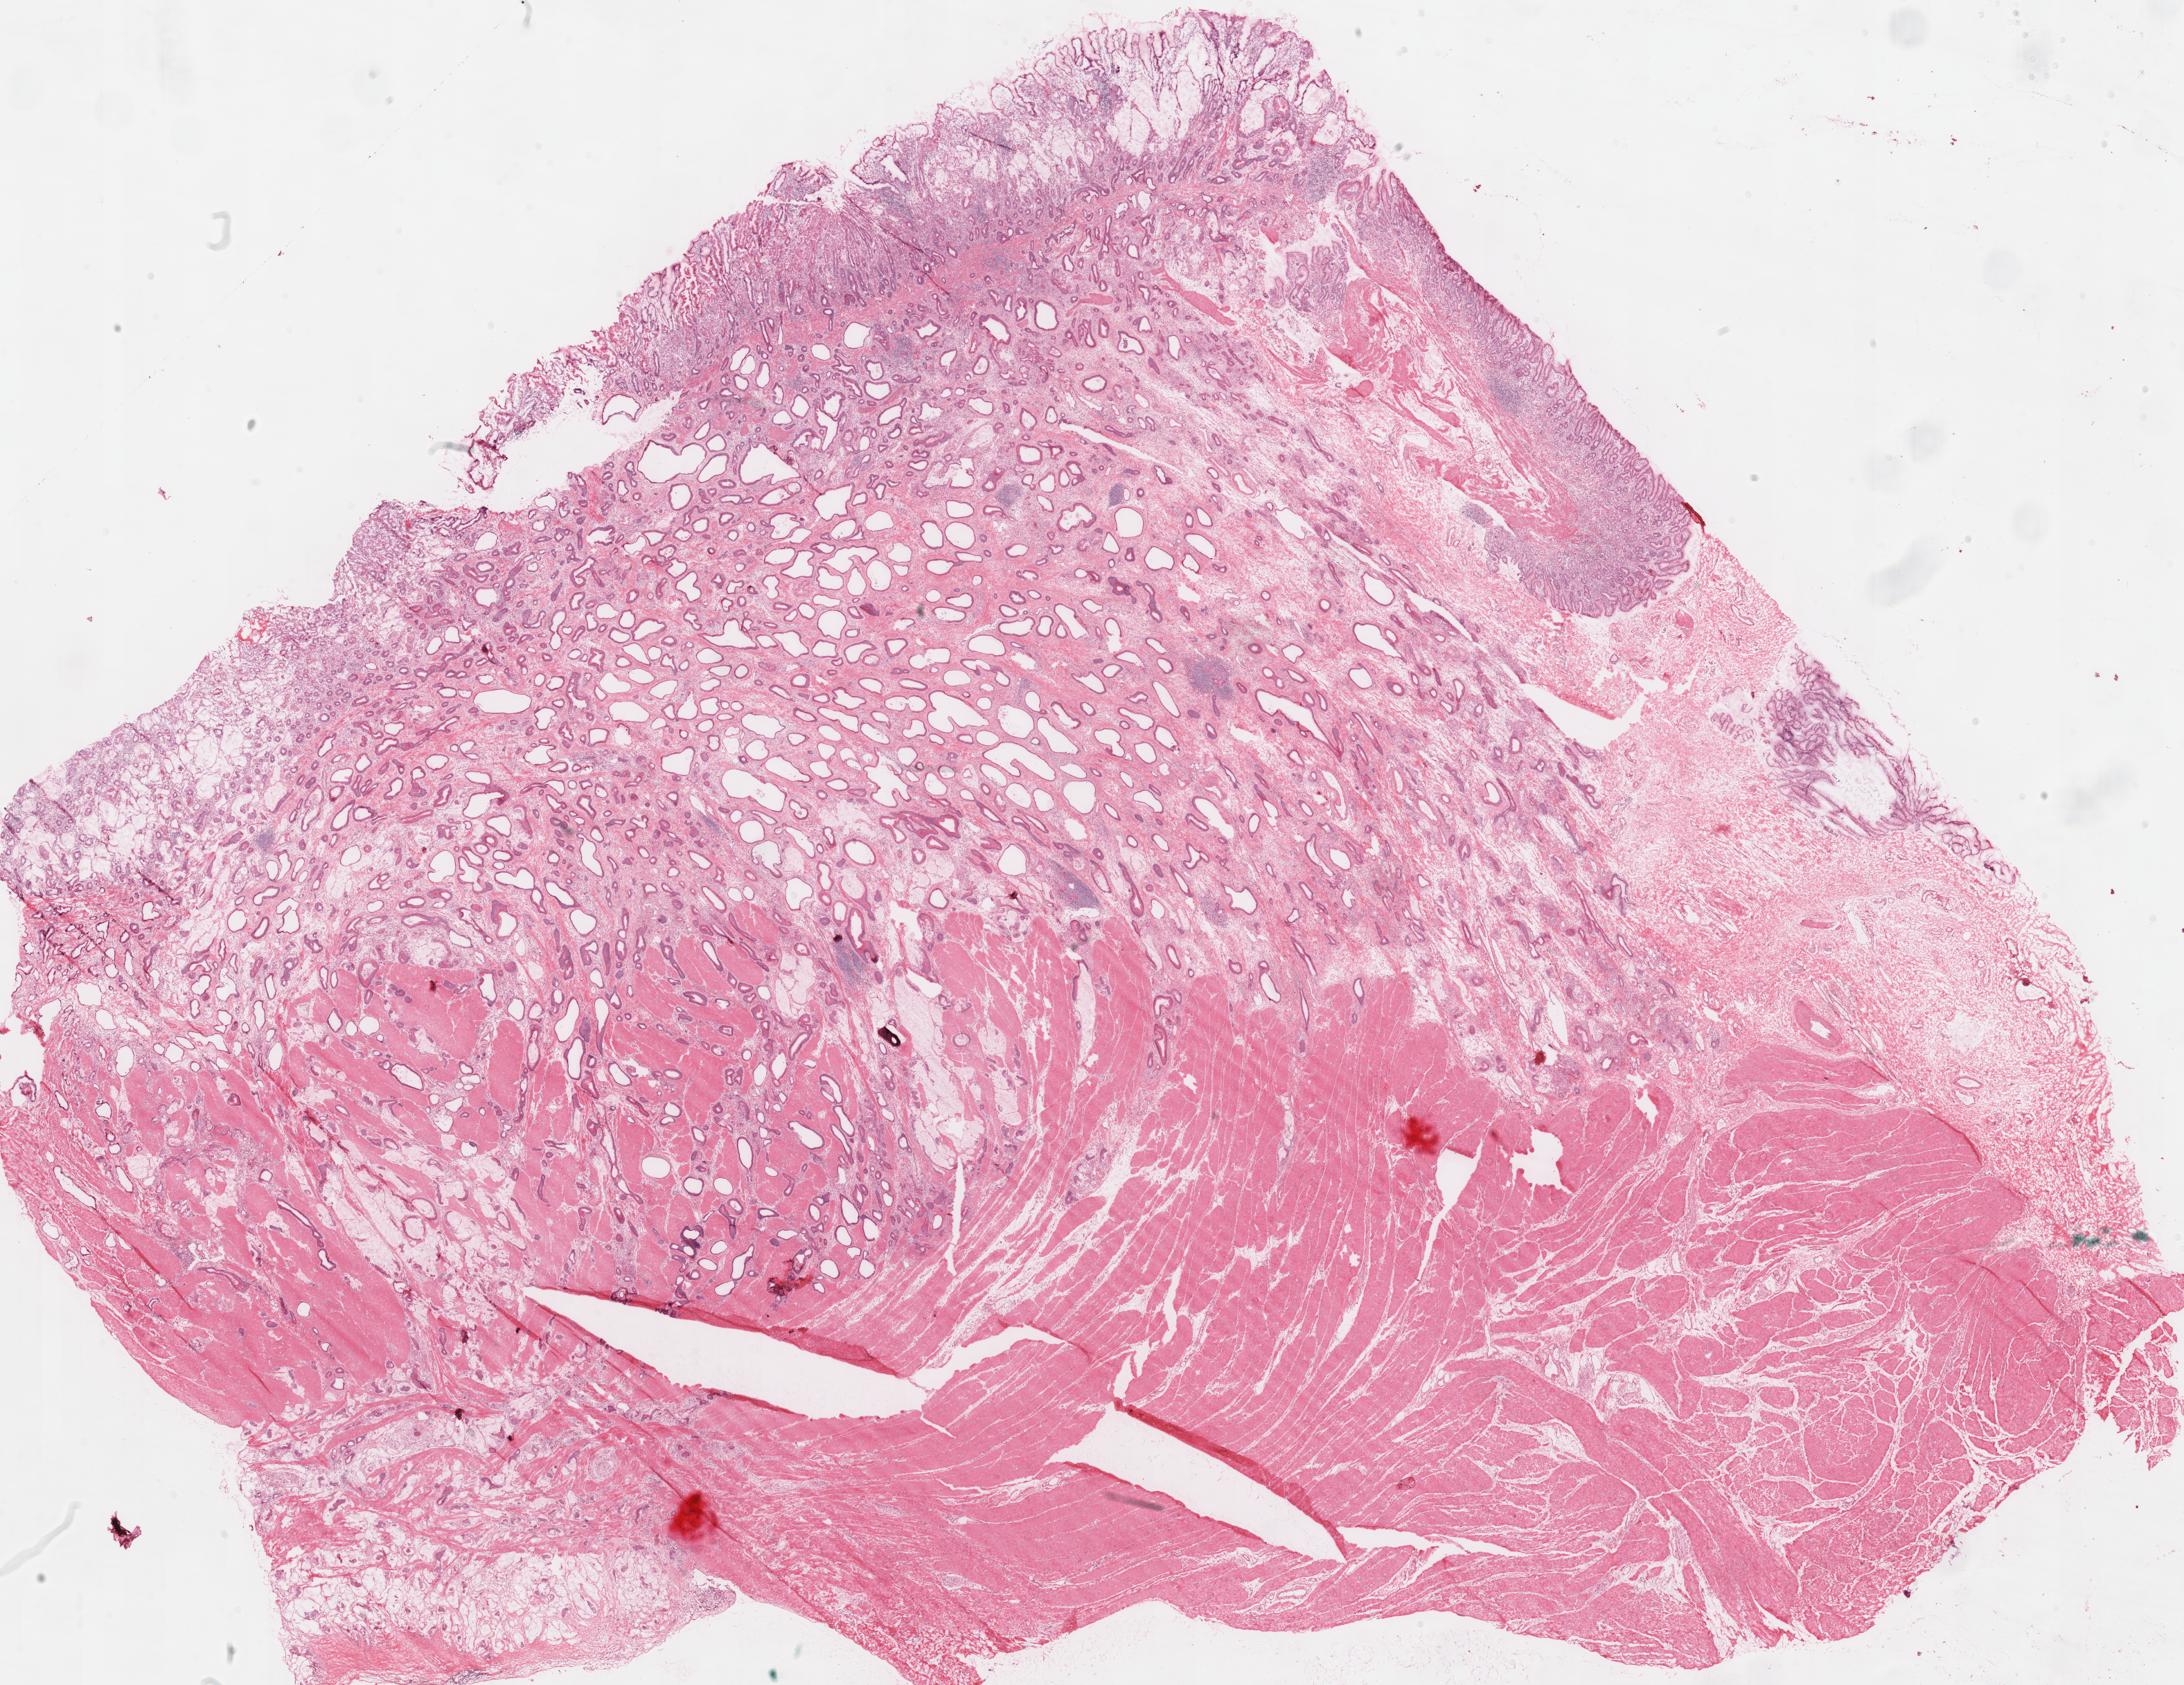
H&E-stained whole-slide image — a low-resolution overview of the entire scanned area, about 24.8 x 19.2 mm, frozen section from the top of the tissue portion, stomach, primary tumour sample. Patient: male, age at initial diagnosis 52 years. Histologic grade: G3 (poorly differentiated). Pathologist review of this section (percent, as recorded): tumour cells 65%, tumour nuclei 80%, normal cells 35%, stromal cells 0%, necrosis 0%. Infiltration values recorded for this section: lymphocyte infiltration 5%, monocyte infiltration 0%, neutrophil infiltration 5%.
Pathologic diagnosis: Mucinous adenocarcinoma (gastric antrum). AJCC pathologic stage: IIB (7th edition).